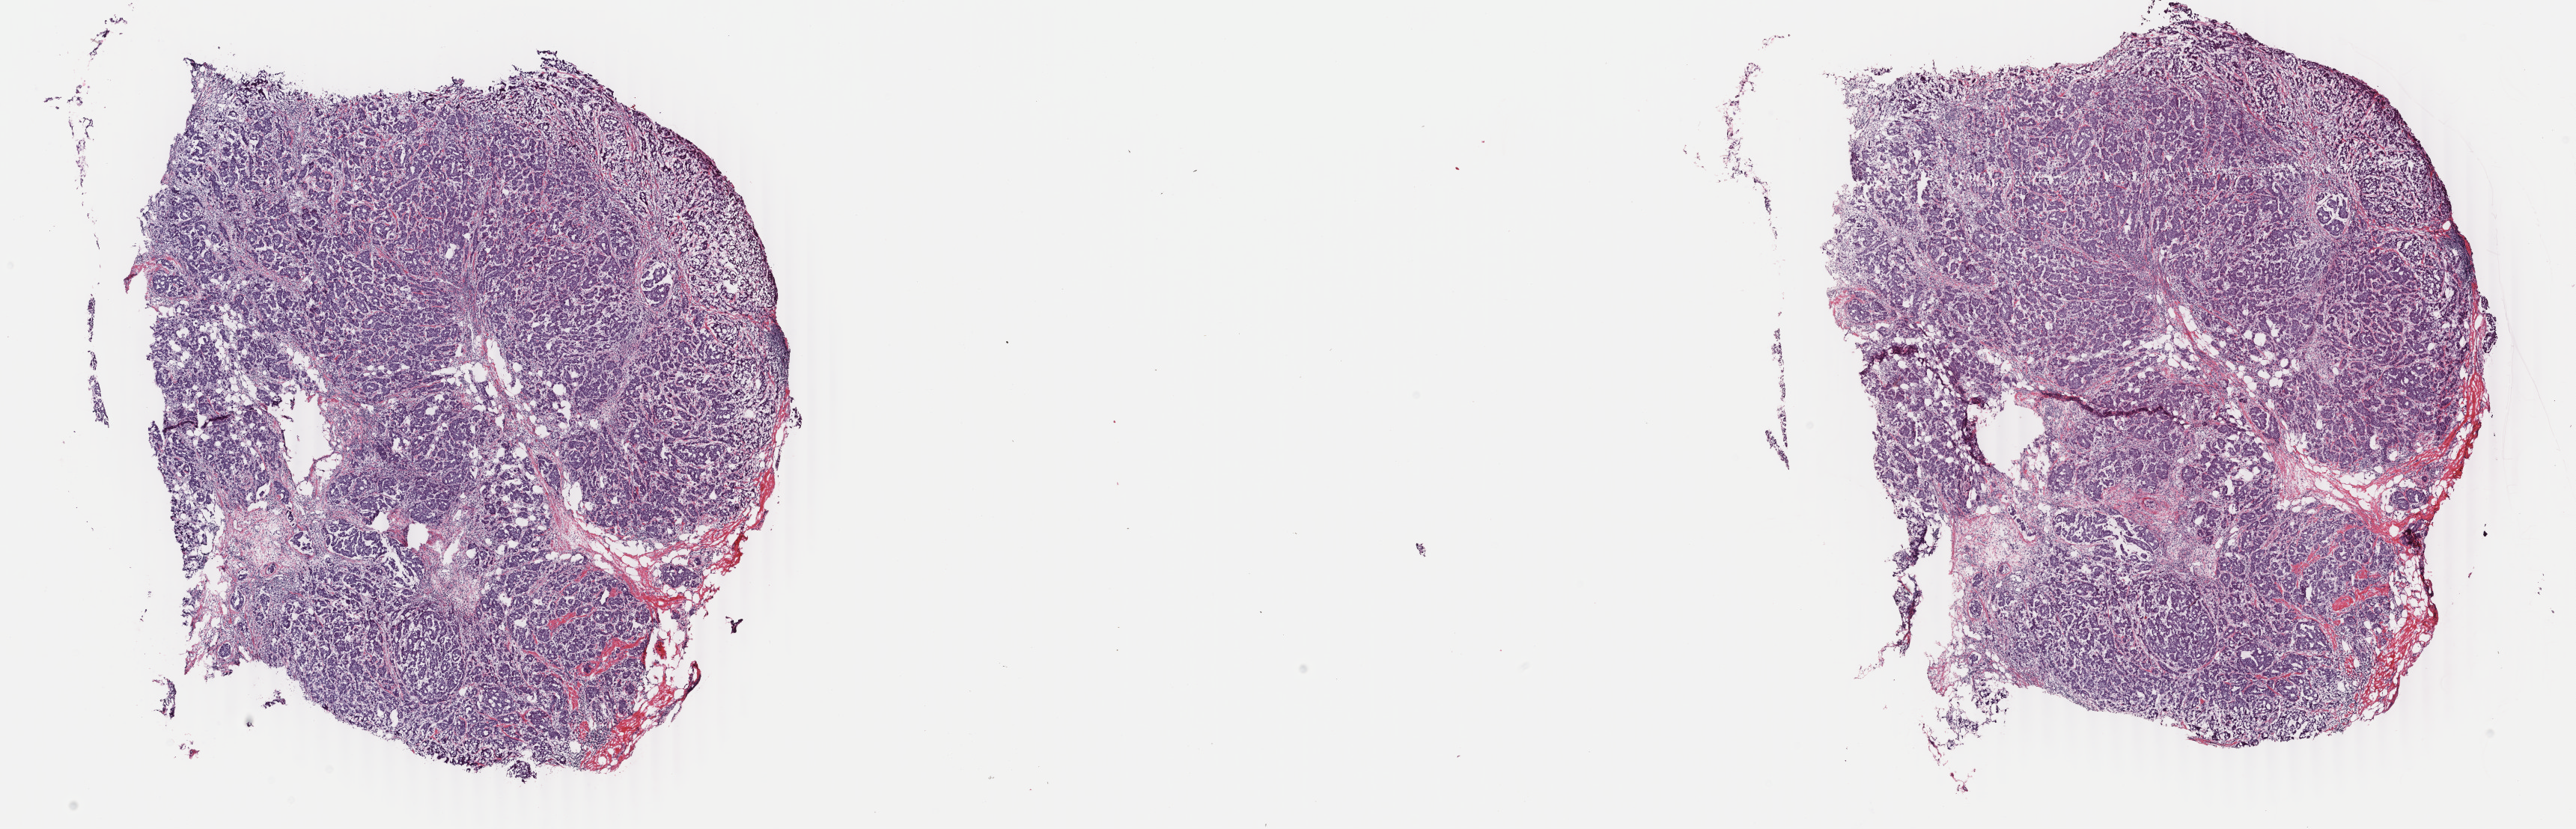
Whole-slide histology image, Hematoxylin and eosin (H&E) stained, whole scanned area (about 27.4 x 8.8 mm) shown as a low-resolution overview. Frozen section from the top of the tissue portion. Sample: primary tumour, breast. Female patient; age at initial diagnosis 27 years. Composition of this section per pathologist review: tumour cells 80%, tumour nuclei 70%, normal cells 0%, stromal cells 20%, necrosis 0%. Infiltration values recorded for this section: lymphocyte infiltration 0%, monocyte infiltration 0%, neutrophil infiltration 0%.
- AJCC pathologic stage: IIIA (6th edition)
- histologic diagnosis: Infiltrating duct carcinoma, NOS